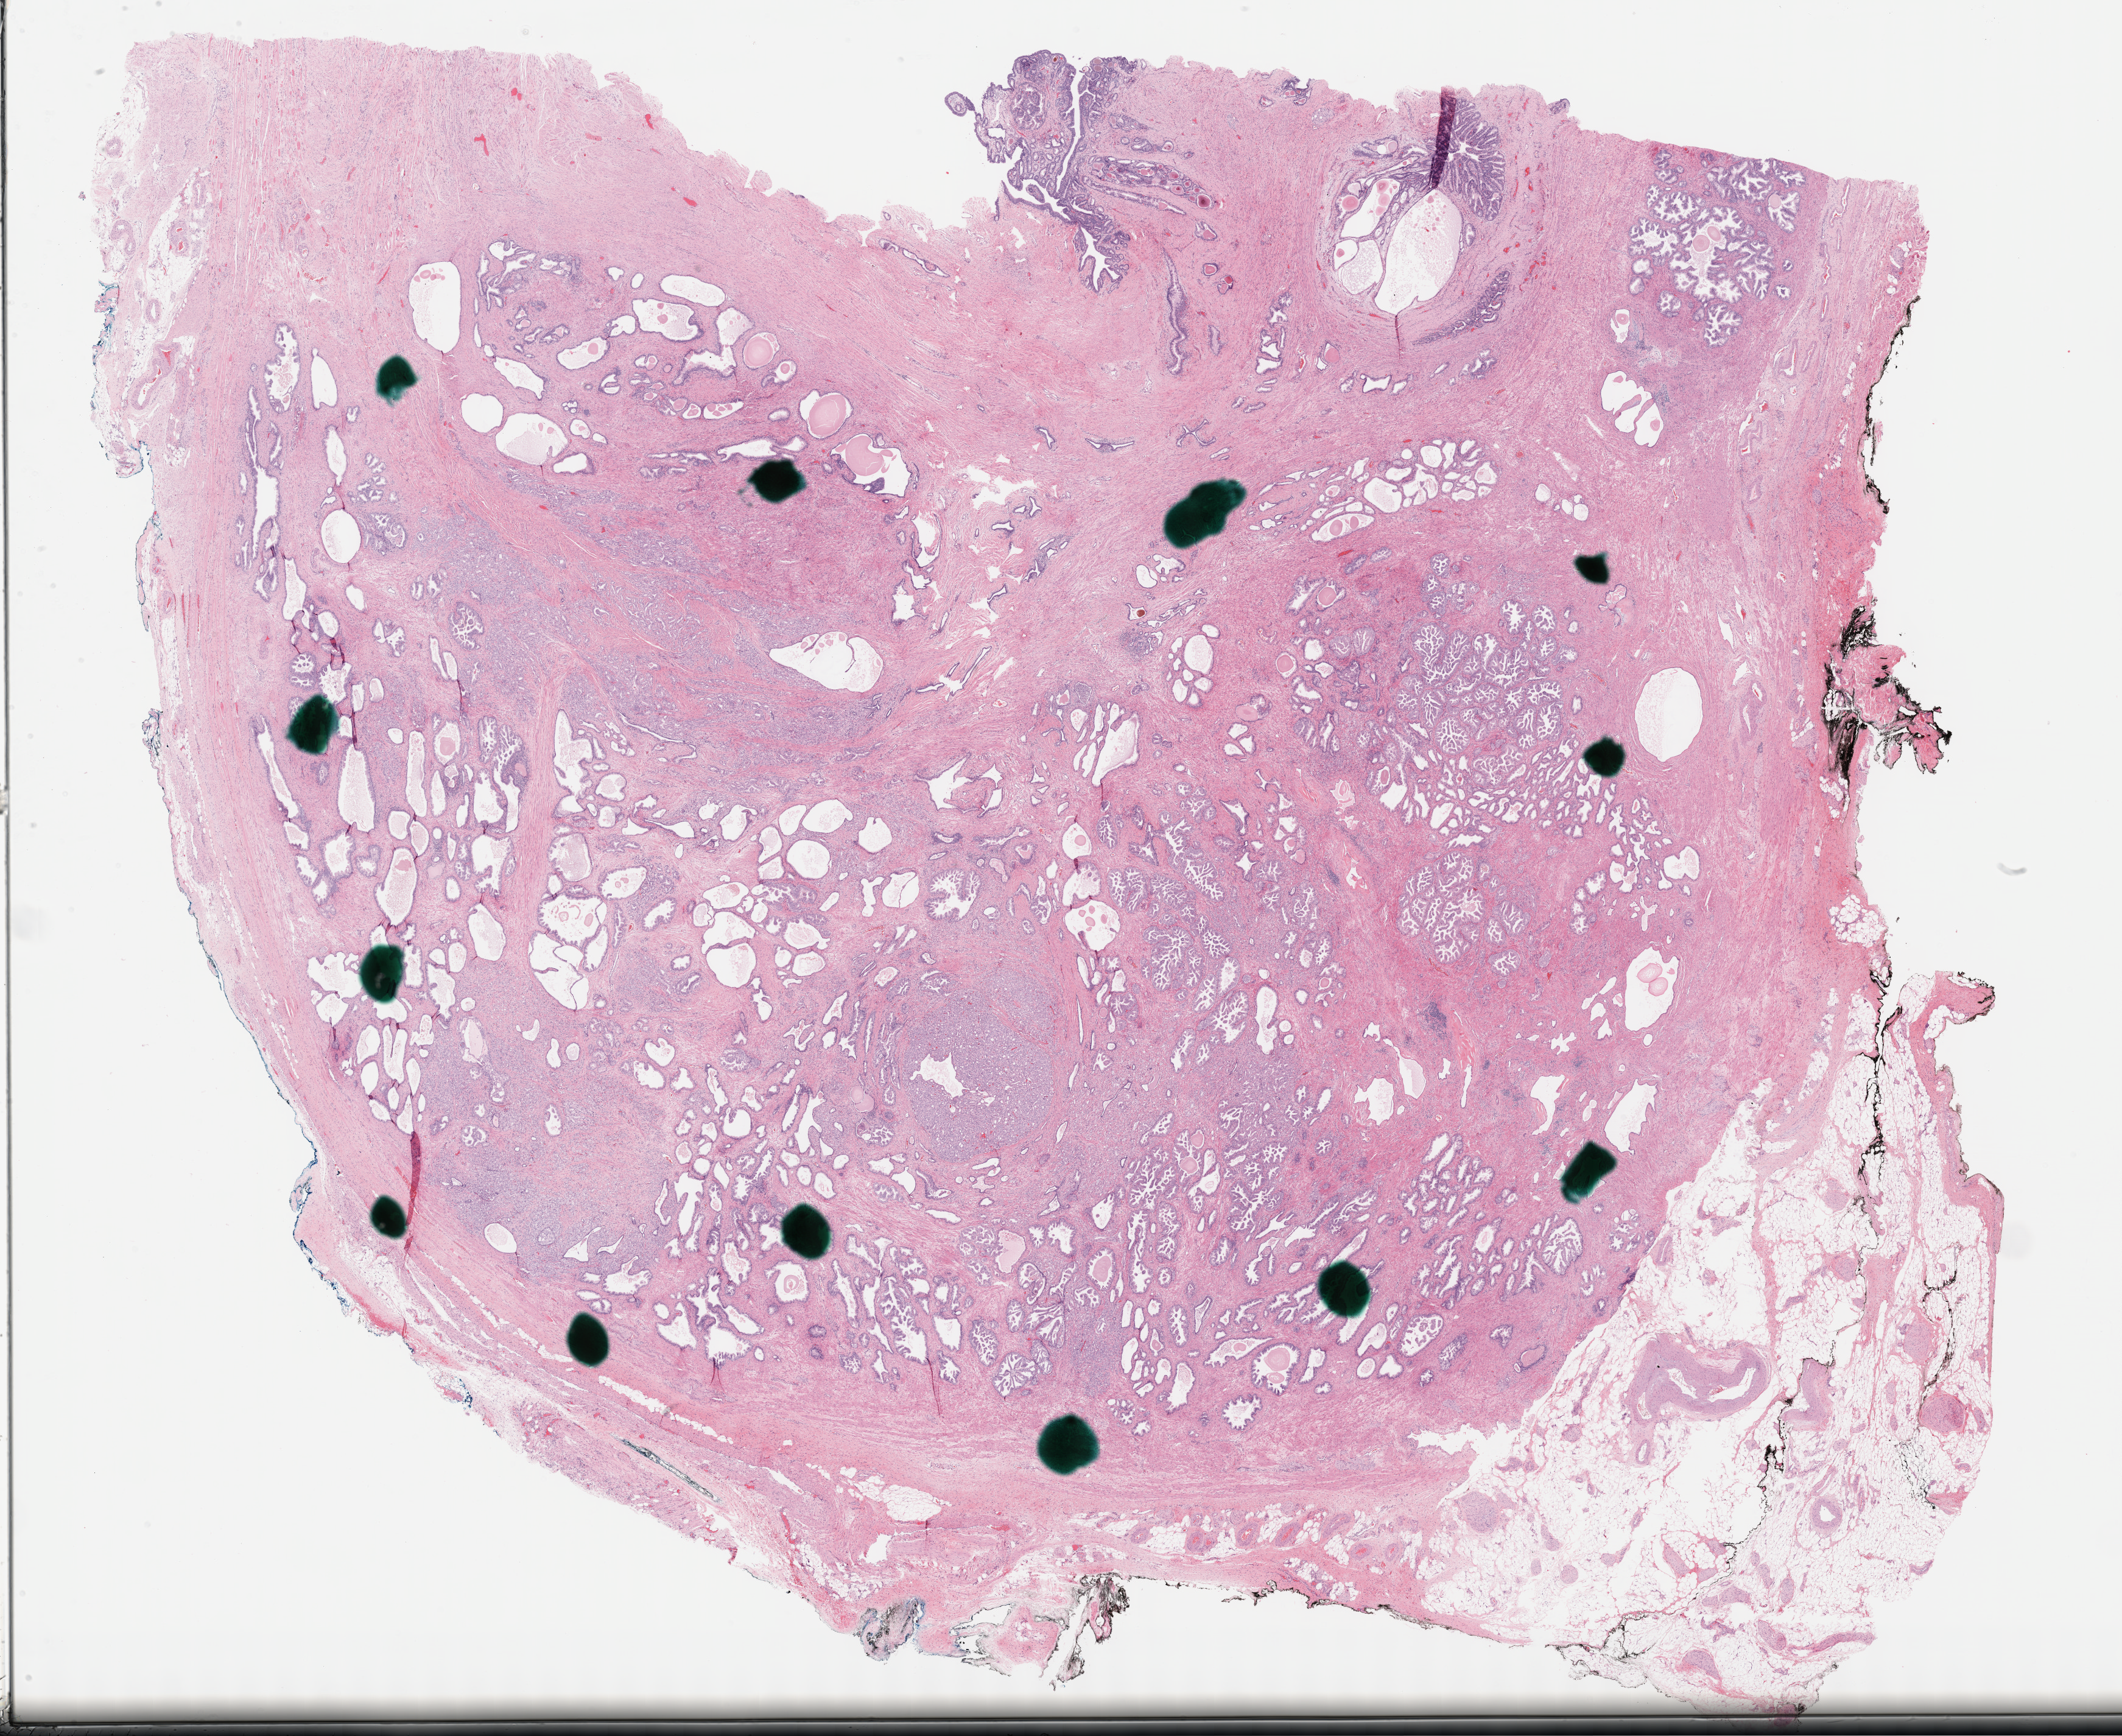
Whole-slide histology image, Hematoxylin and eosin (H&E) stained — shown as a low-resolution overview of the whole scanned area (about 28.2 x 23.1 mm, slide scanned at 40x); FFPE section; sample: primary tumour, prostate. Patient: male, age at initial diagnosis 63 years. Gleason score: 9 (4+5).
Laterality: bilateral. Lymph nodes positive (case pathology): 0 of 29 examined. Diagnosis: Adenocarcinoma, NOS (prostate gland).